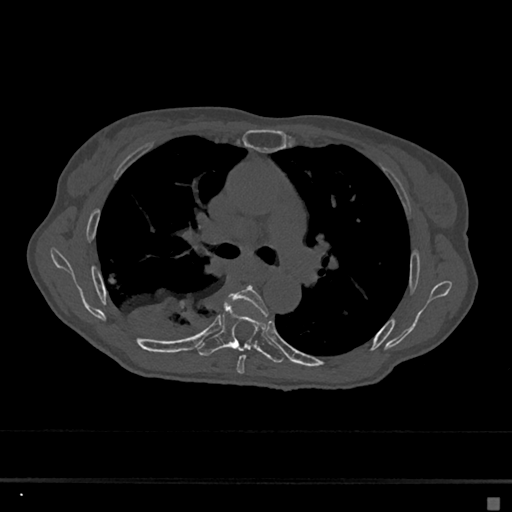
CT including the spine, one axial slice. Position 435 of 797 along the scan axis. Reconstruction kernel Br40s/3. Bone window (W 1800 / L 400 HU). 0.5 mm slice thickness. 512 × 512 image matrix, field of view 360 × 360 mm. Female patient, age 68 years. Case-level facts recorded for this patient, not image findings: primary cancer: renal.
Annotated regions visible in this slice (semi-automatically segmented with operator editing):
- T5 vertebra: box from (x=227, y=285) to (x=268, y=374) px
- T6 vertebra: (x=197, y=300)–(x=284, y=363)